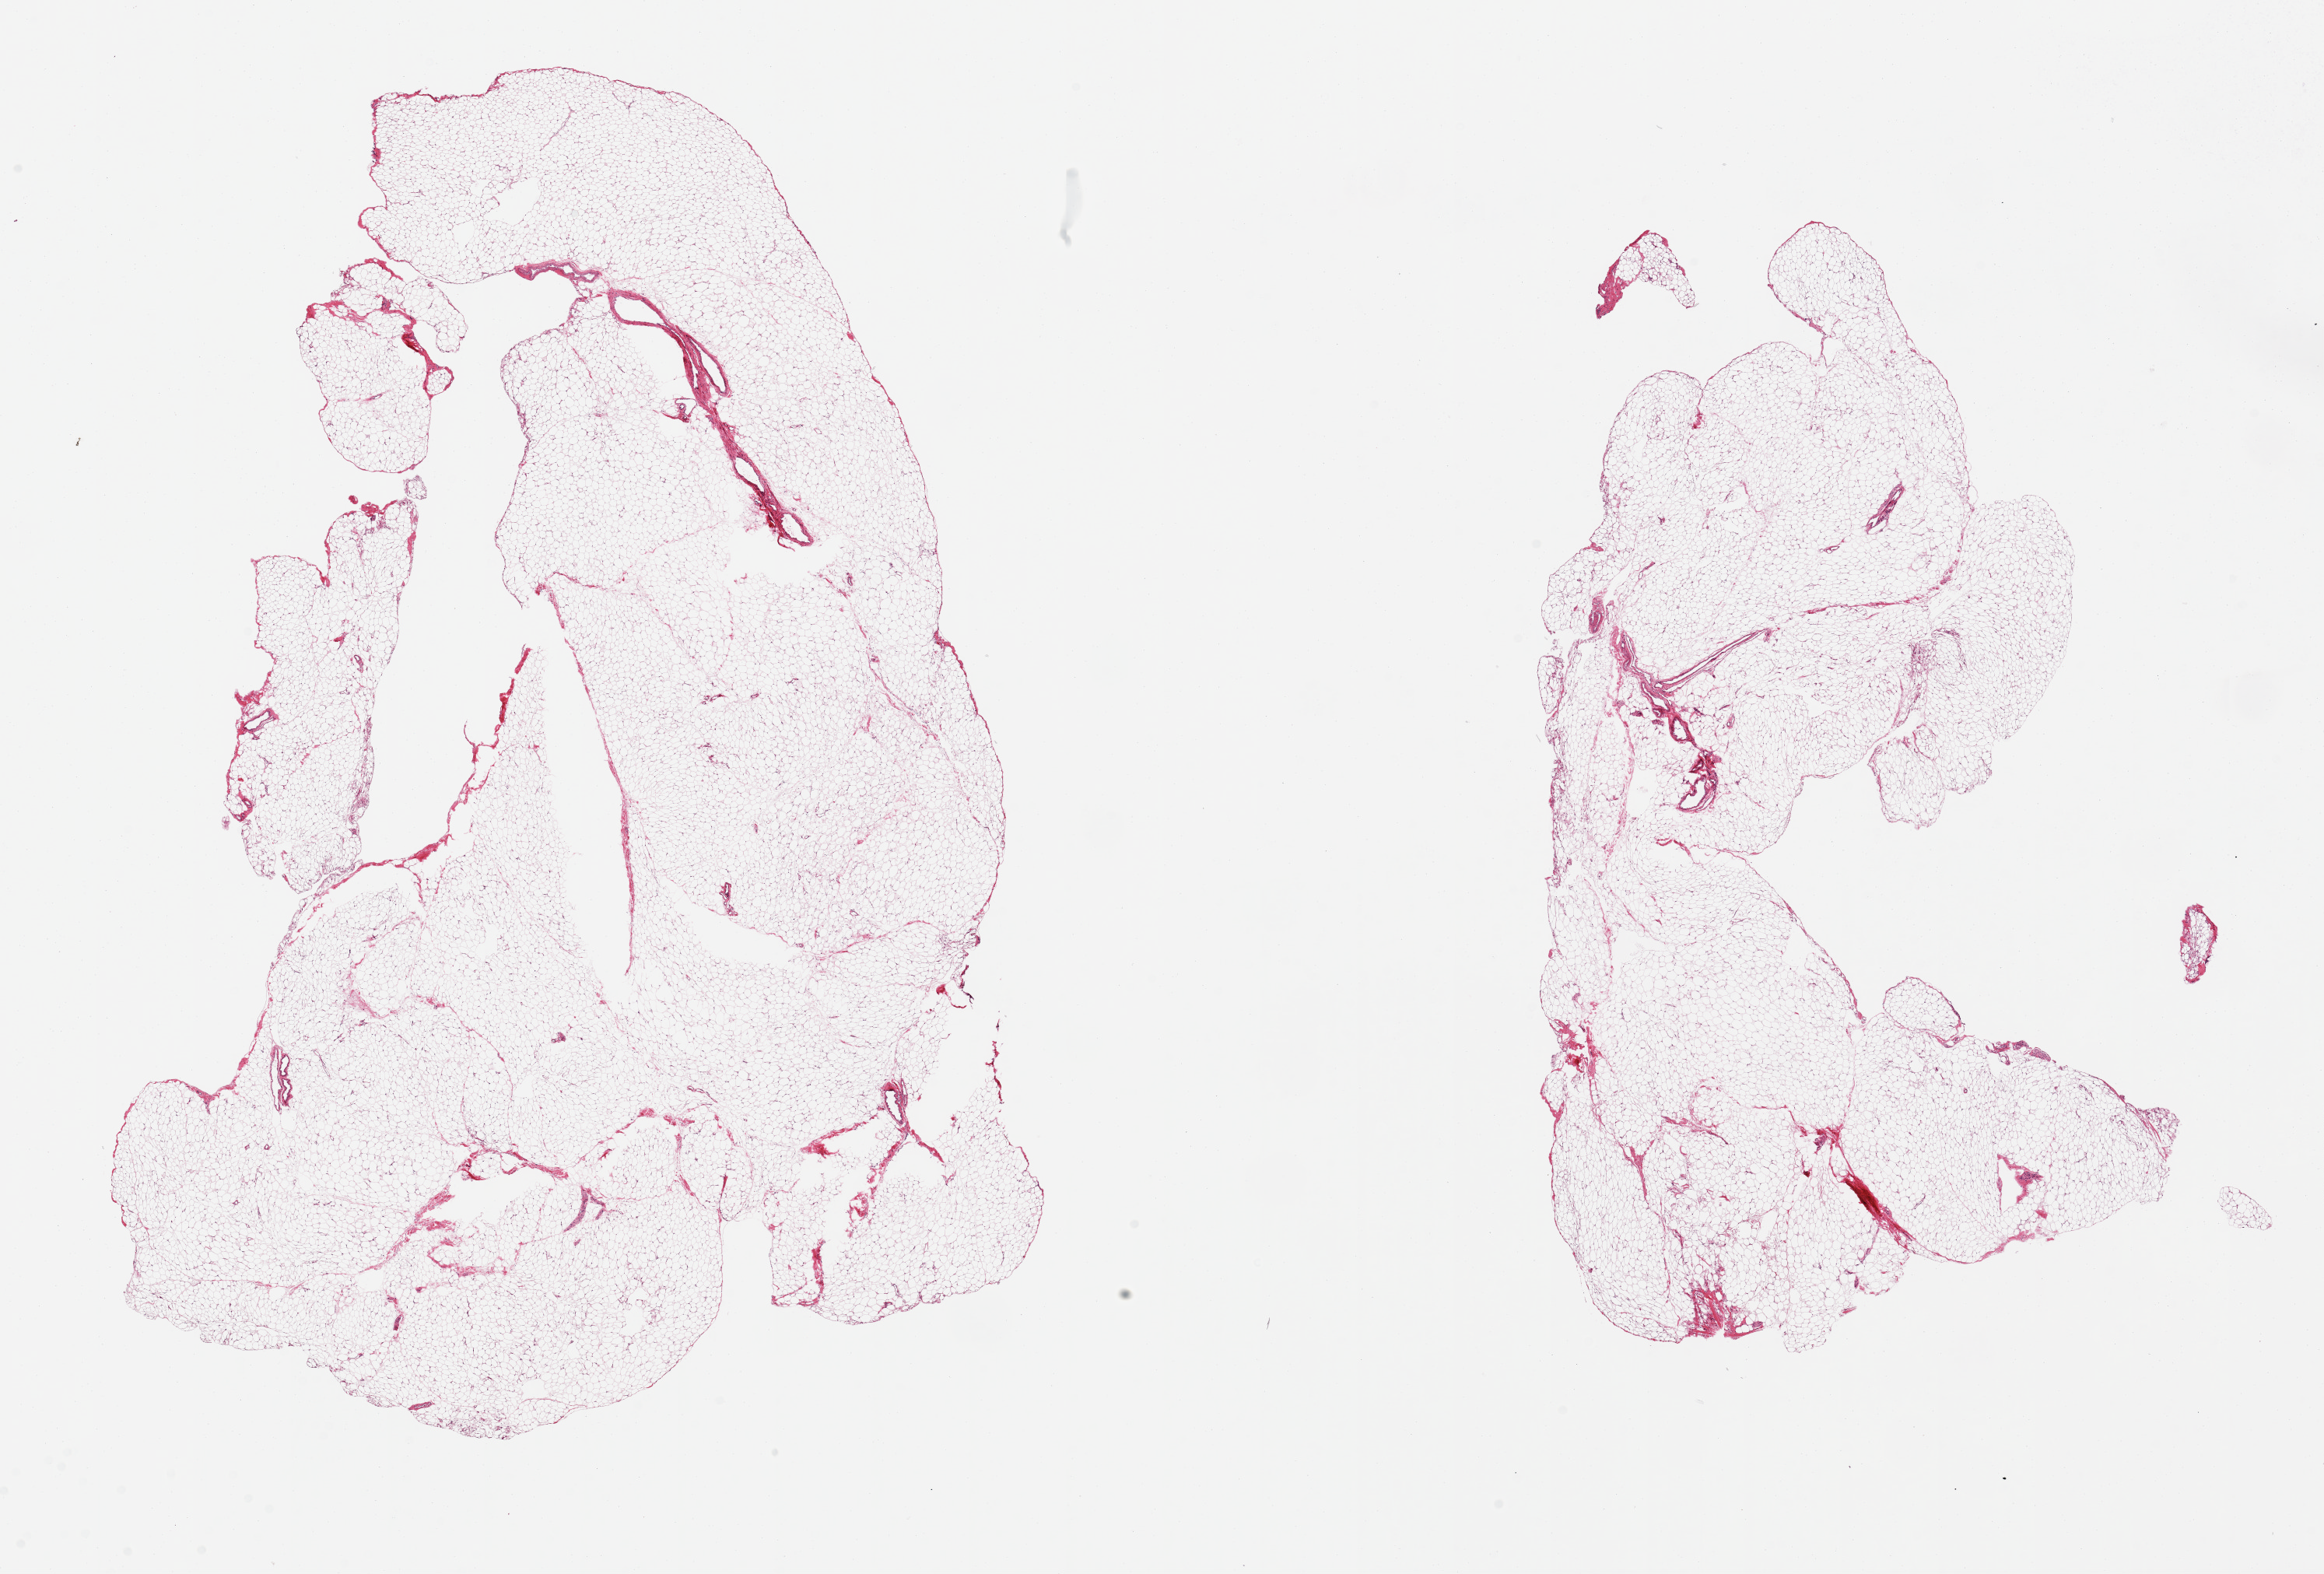
Whole-slide image, H&E stain, brightfield, a low-resolution overview of the entire scanned area, about 23.6 x 16.0 mm (from a 20x scan). PAXgene-fixed, paraffin-embedded tissue. Section of omentum (target tissue). Tissue donor sample. Donor sex: female.
Pathologist's review note for this sample: 2 pieces.